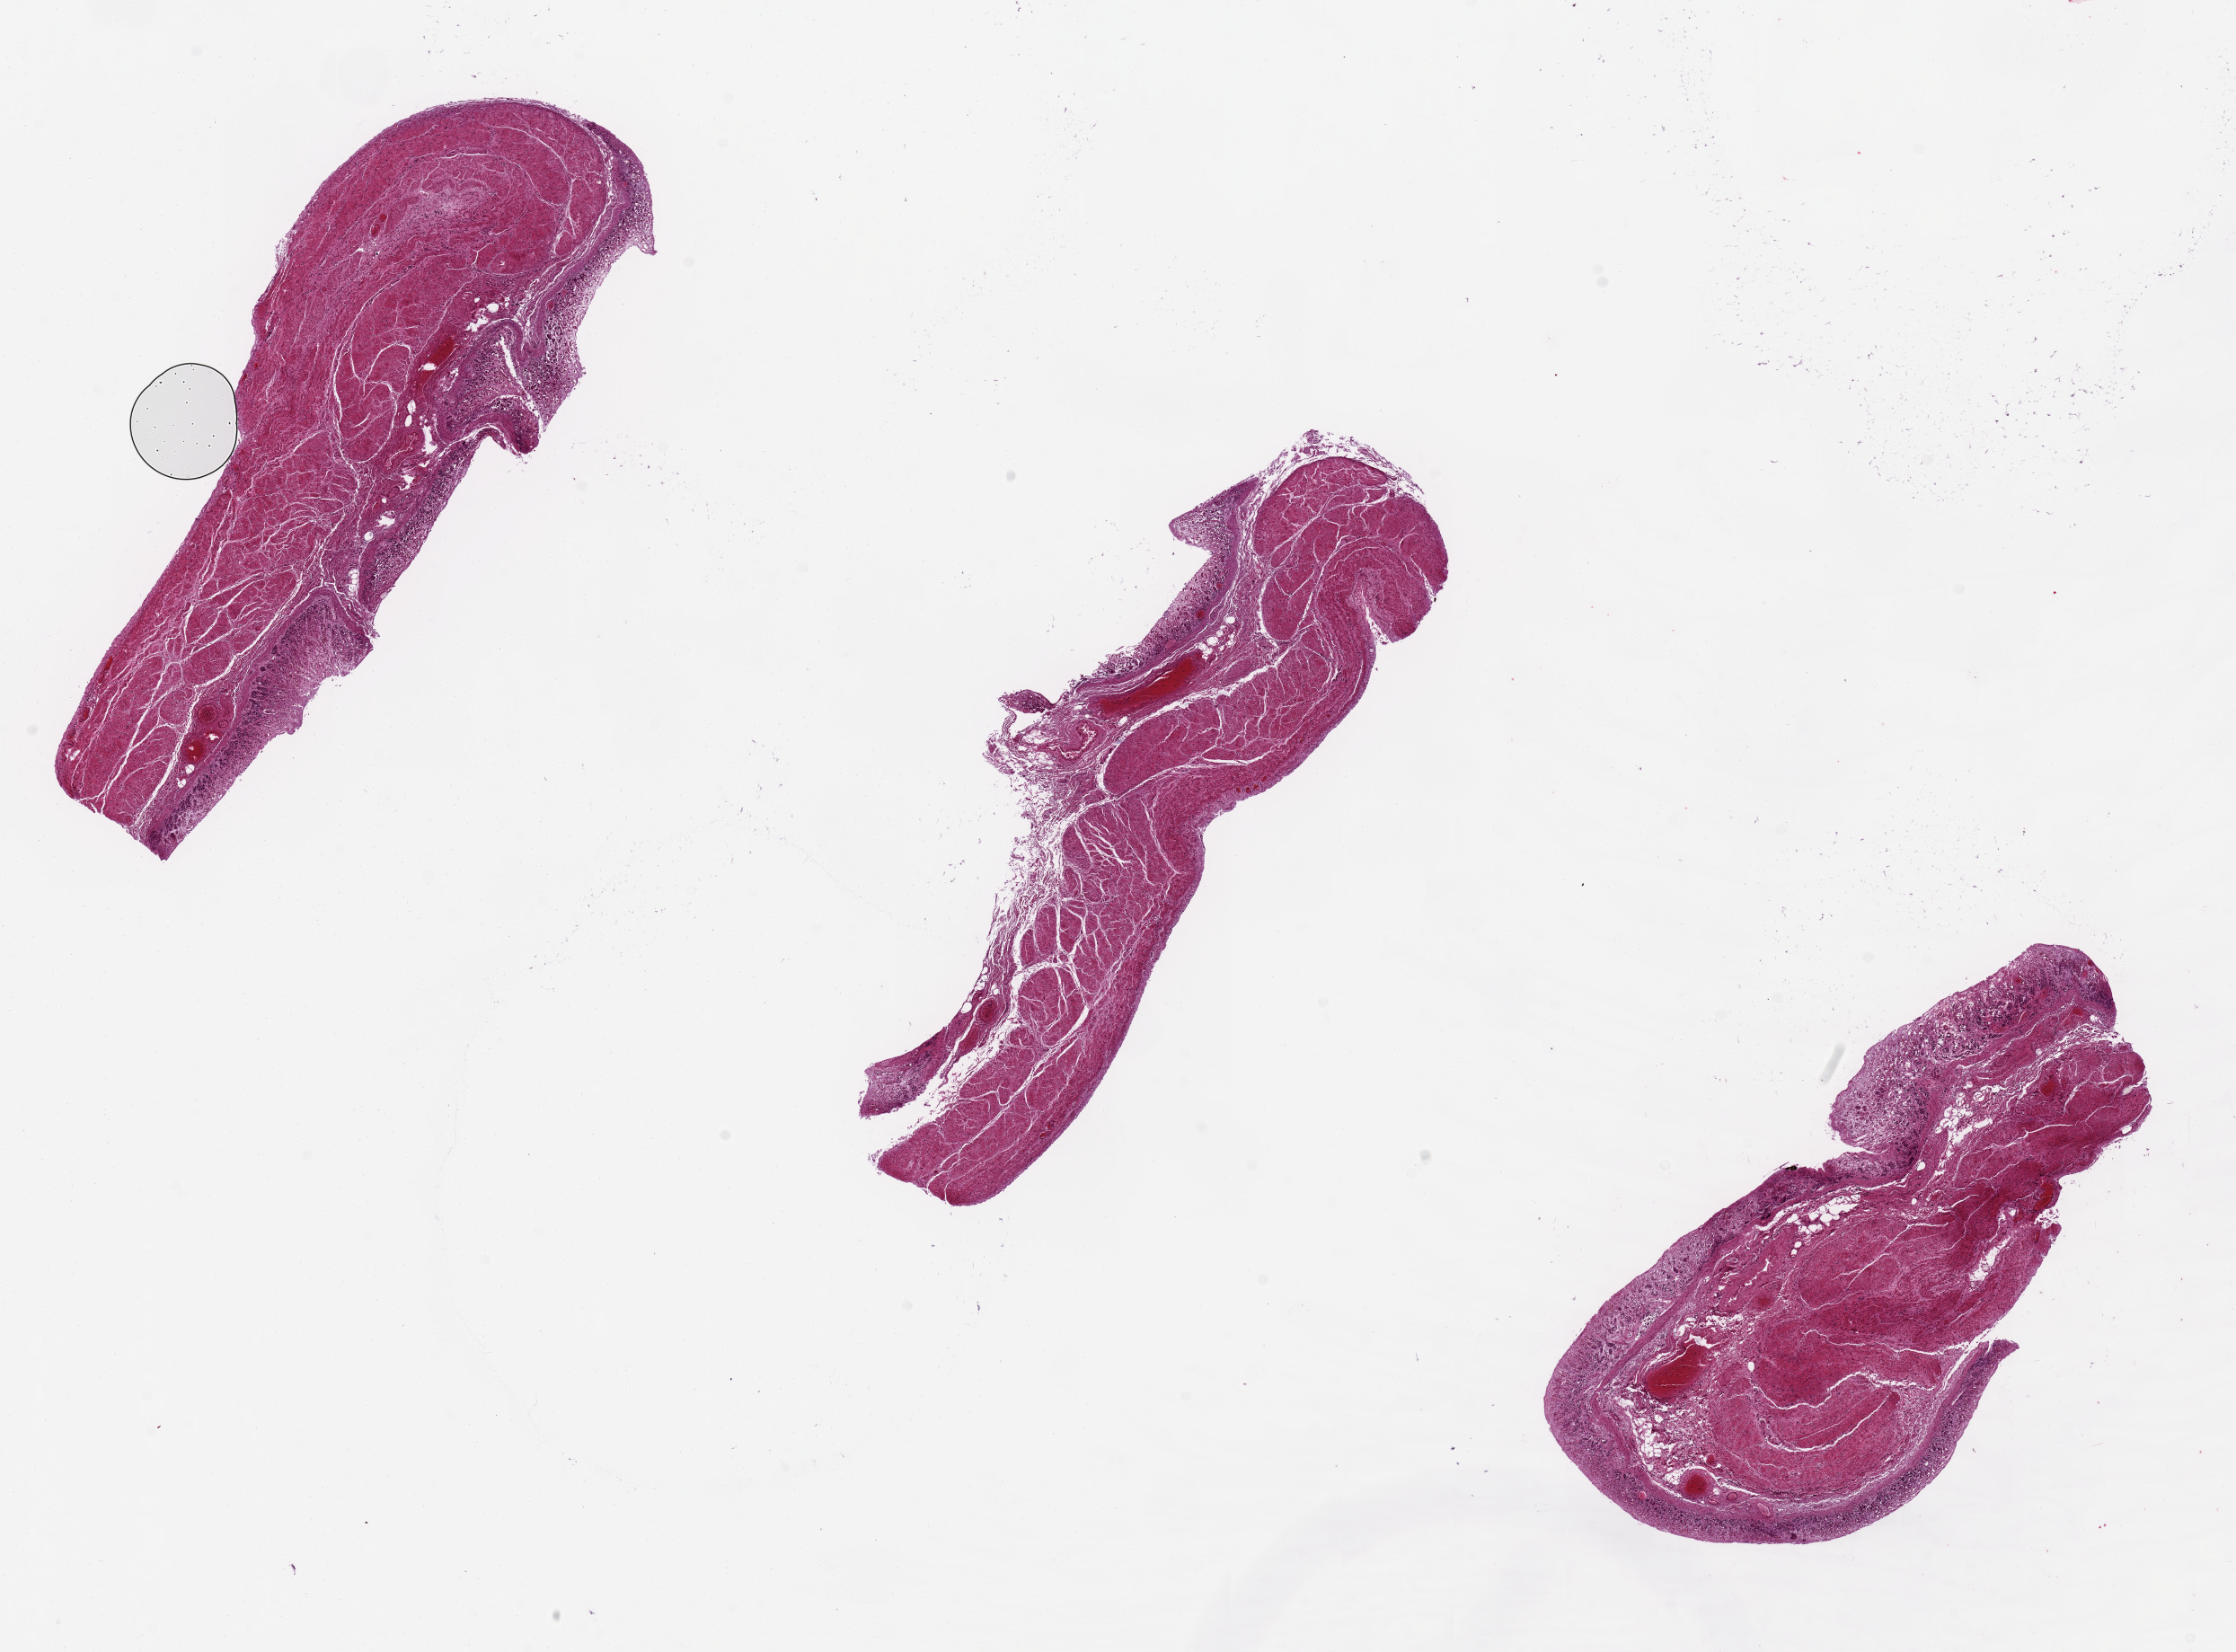
Hematoxylin and eosin (H&E) whole-slide image, whole scanned area (about 19.7 x 14.5 mm) shown as a low-resolution overview, PAXgene-fixed paraffin-embedded (PFPE) section, sampled site (target tissue): stomach, donor tissue sample. Female donor.
Reviewer comment on this tissue sample: Mucosa totally autolyzed; wall.